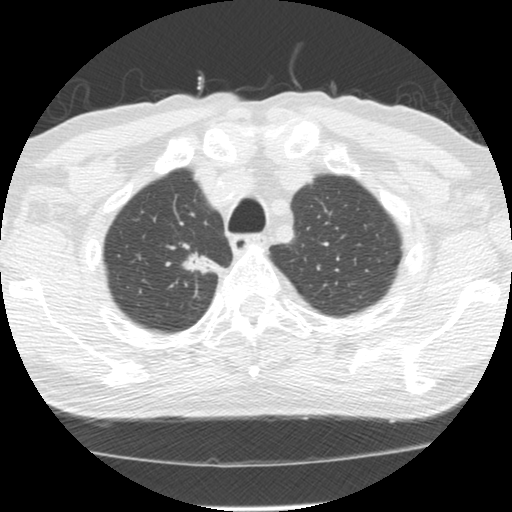
Low-dose screening chest CT, one axial slice. Slice 113 of 139 in the series (ordered by position). Lung window (W 1500 / L -600 HU). 2.5 mm slice thickness. 512 × 512 image matrix, field of view 310 × 310 mm.
Outlined on this slice (manually delineated by an expert):
- lesion 1 (tumor, upper lobe of right lung): bounding box [x1, y1, x2, y2] px = [182, 252, 219, 275]